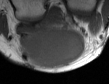
MRI of an extremity soft-tissue mass, one axial slice. Position 18 of 50 along the scan axis. MR volume resampled by the dataset authors to the PET/CT grid (not the native acquisition matrix). 3.27 mm slice thickness. 109 × 84 image matrix, field of view 106 × 82 mm. Male patient. Case-level facts recorded for this patient, not image findings: histological type: synovial sarcoma; site of the primary tumour: left poplietal fossa.
Annotated regions visible in this slice (expert contour drawn on MRI and transferred to this co-registered scan by the dataset authors):
- gross tumour volume (mass): bounding box (x1, y1, x2, y2) in pixels: (18, 26, 85, 68)